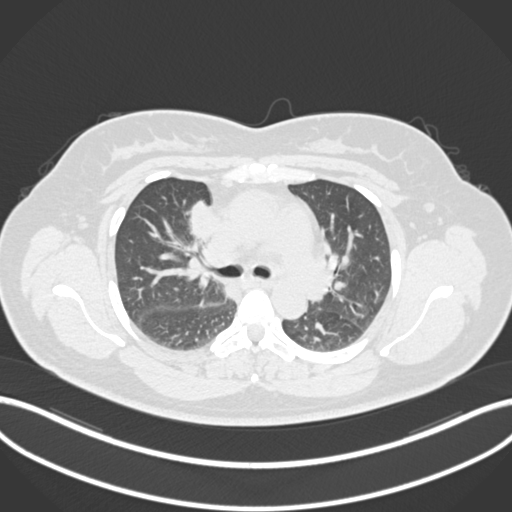
Chest CT, one axial slice. Position 114 of 183 along the scan axis. Reconstruction kernel B30f. 120 kVp. Lung window (W 1500 / L -600 HU). 1 mm slice thickness. 512 × 512 image matrix, field of view 400 × 400 mm. Patient: female, 46 years. From the clinical record (not read from this slice): clinical TNM (as recorded): T2a N1 M0.
Annotated regions visible in this slice (rectangle marked by the reading radiologist):
- lung tumour (recorded histology: adenocarcinoma): box from (x=182, y=200) to (x=215, y=247) px